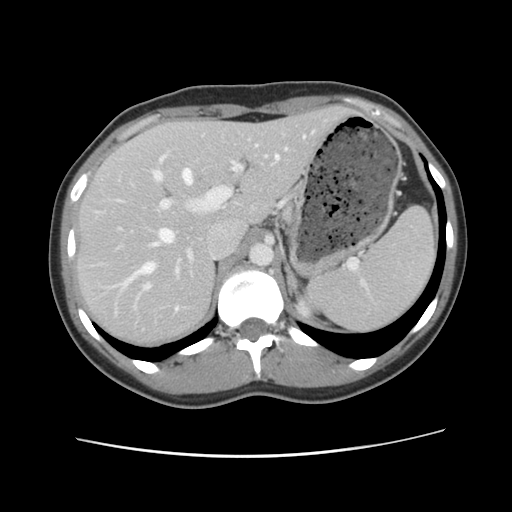
Contrast-enhanced abdominal CT, one axial slice. Slice 77 of 134 in the series (ordered by position). 120 kVp. Intravenous contrast given. Soft-tissue window (W 400 / L 40 HU). 512 × 512 image matrix, field of view 339 × 339 mm. Female patient, age 33 years. From the clinical record (not read from this slice): diagnosis: colorectal cancer liver metastases, imaged before liver resection; multiple liver metastases: yes; largest metastasis: 4.5 cm; disease in both lobes: yes.
Annotated regions visible in this slice (outlined manually by an expert reader):
- hepatic veins: bounding box [x1, y1, x2, y2] px = [125, 136, 305, 311]
- liver: [78, 108, 350, 348]
- planned liver remnant (the part of the liver to remain after resection): [78, 108, 351, 348]
- portal vein (with intrahepatic branches): [147, 146, 290, 288]